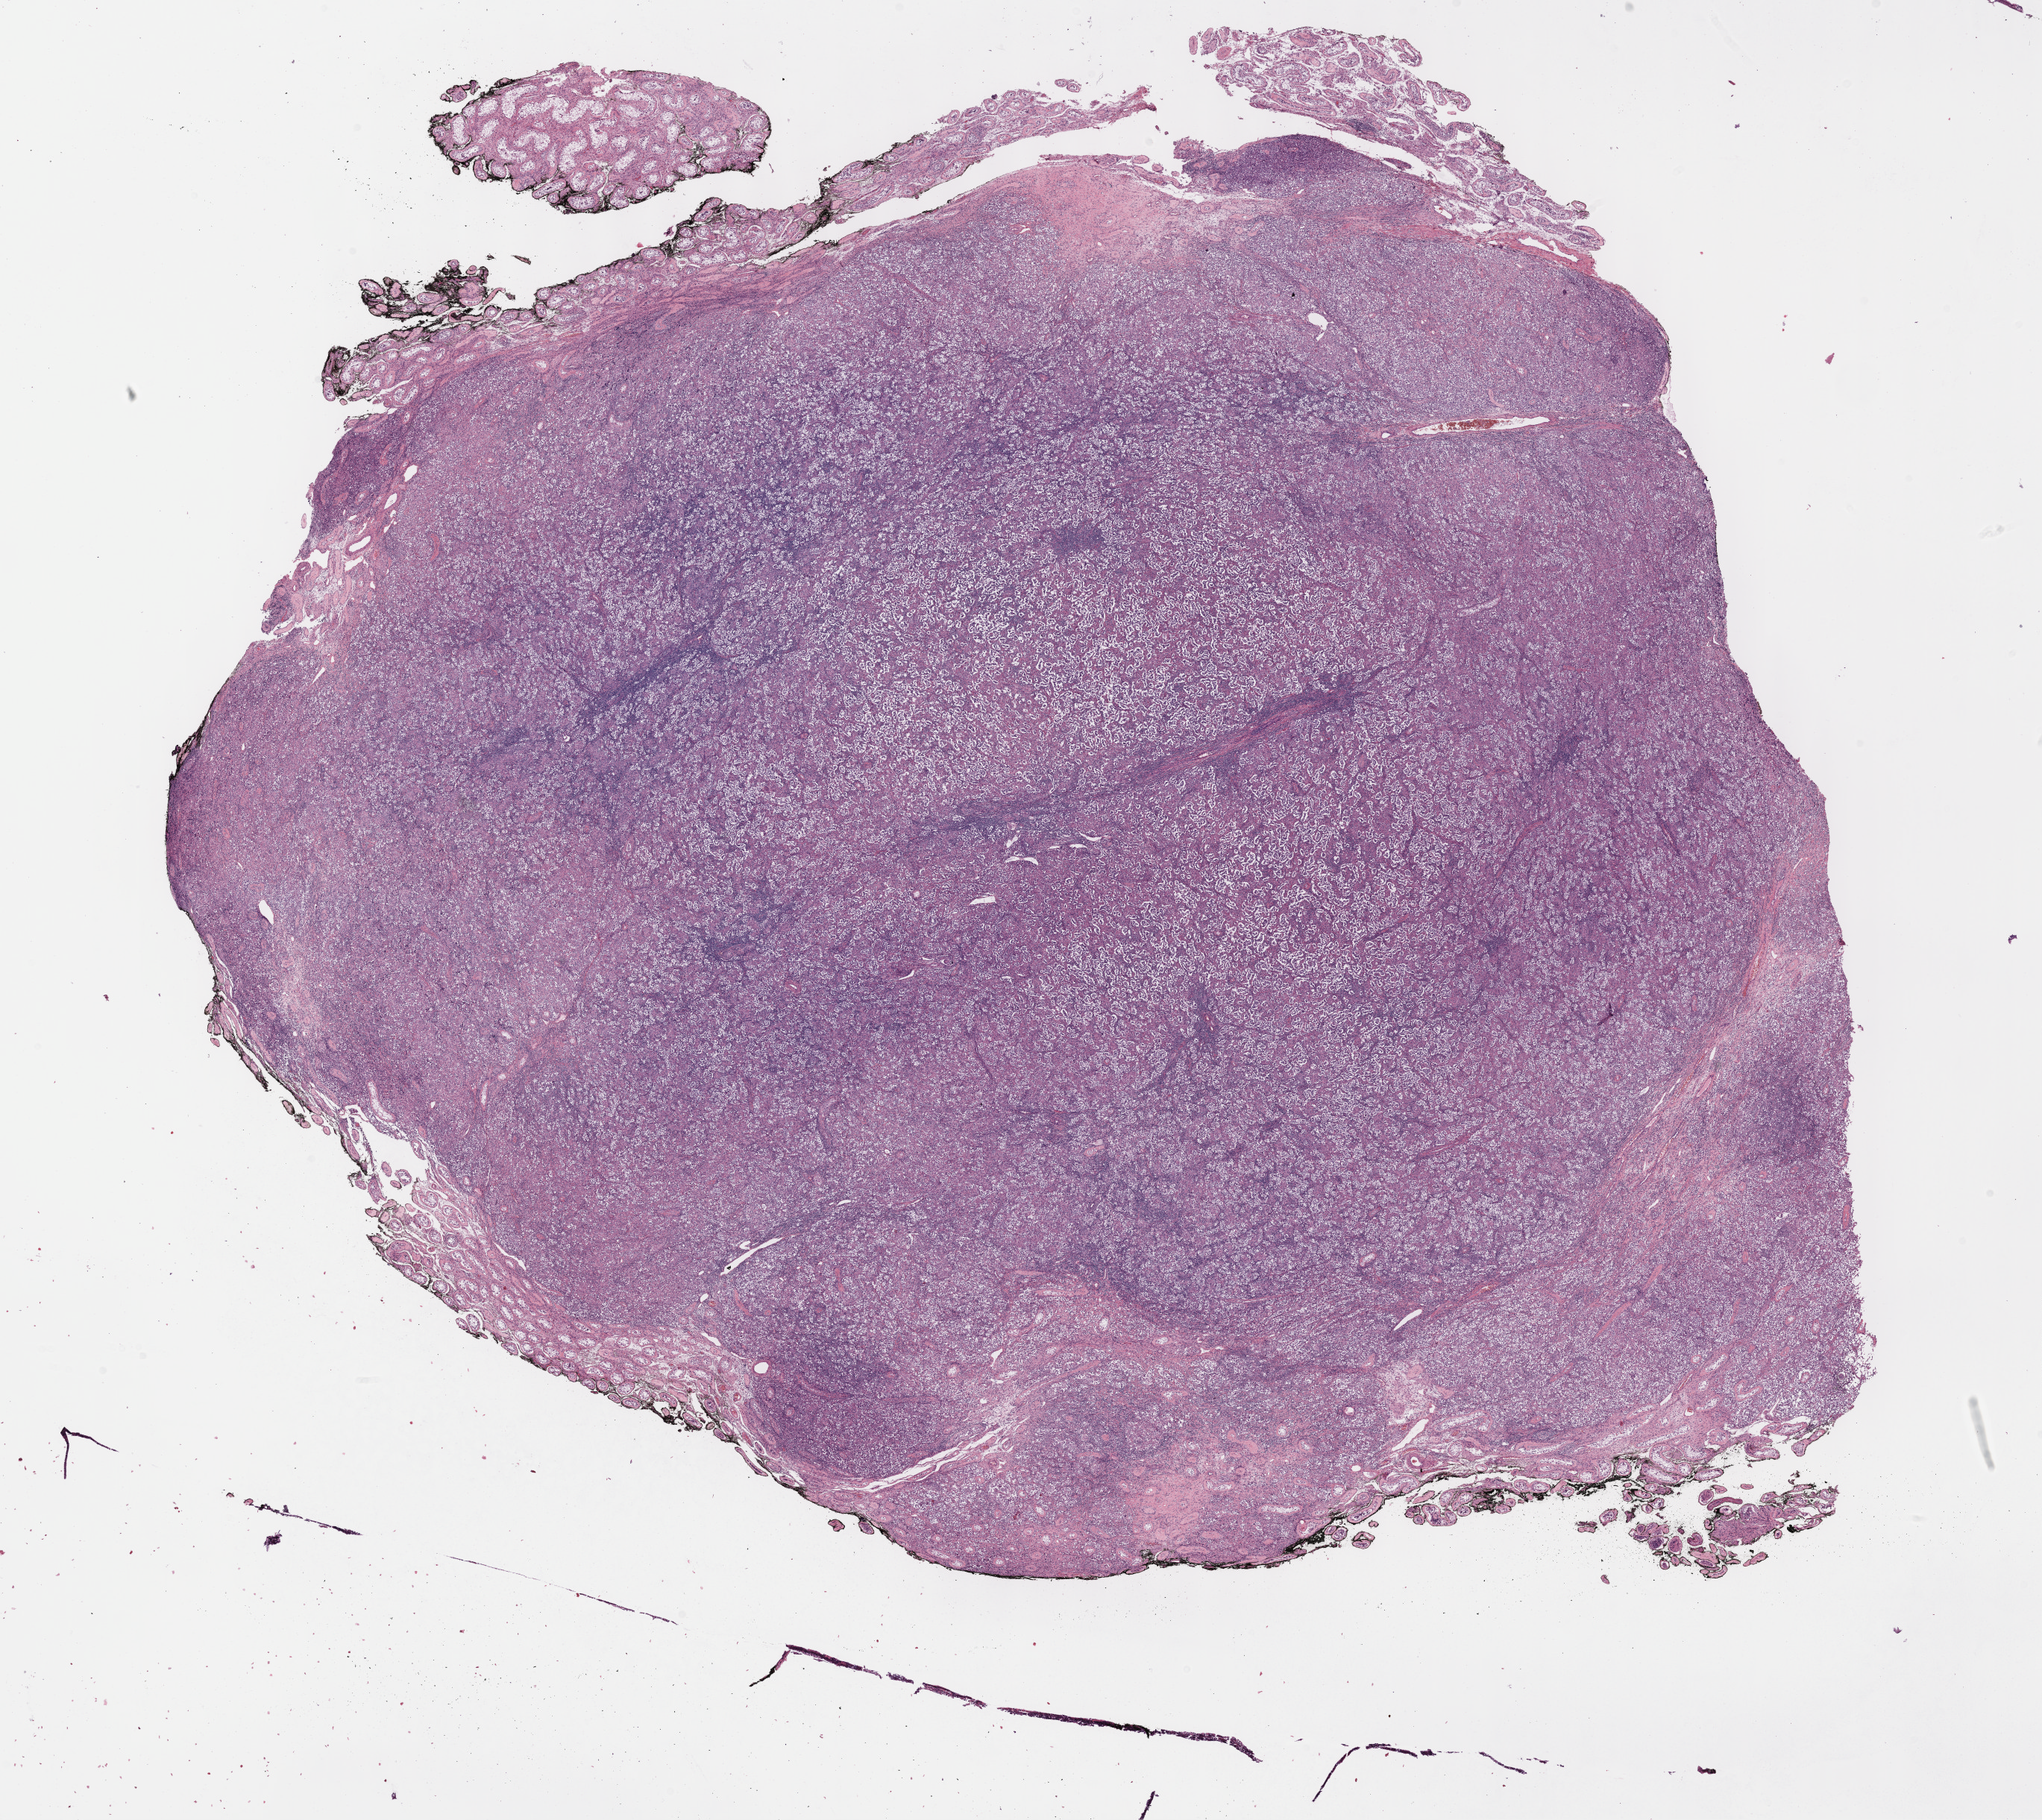
Digitized Hematoxylin and eosin (H&E) stained tissue section (whole slide), shown as a low-resolution overview of the whole scanned area (about 22.1 x 19.7 mm); formalin-fixed paraffin-embedded (FFPE) diagnostic section; testis, primary tumour sample. Male patient; age at initial diagnosis 26 years.
Pathologic diagnosis: Seminoma, NOS.